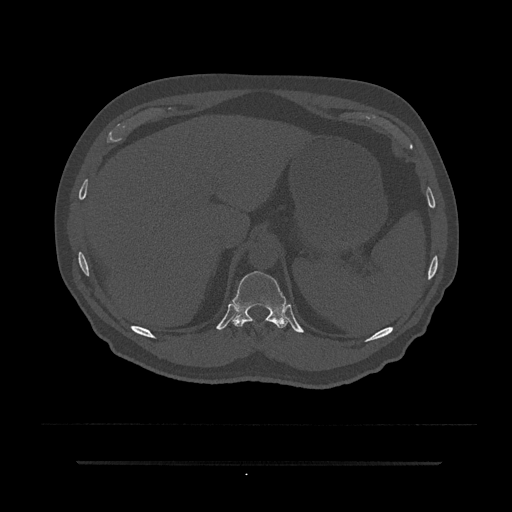
CT including the spine, one axial slice. Slice 284 of 797 in the series (ordered by position). Bone window (W 1800 / L 400 HU). 512 × 512 image matrix, field of view 464 × 464 mm. Patient: male, 59 years. From the clinical record (not read from this slice): primary cancer: bile ducts.
Outlined on this slice (semi-automatically segmented with operator editing):
- T11 vertebra: bounding box <231,271,290,329> (left, top, right, bottom; pixels)